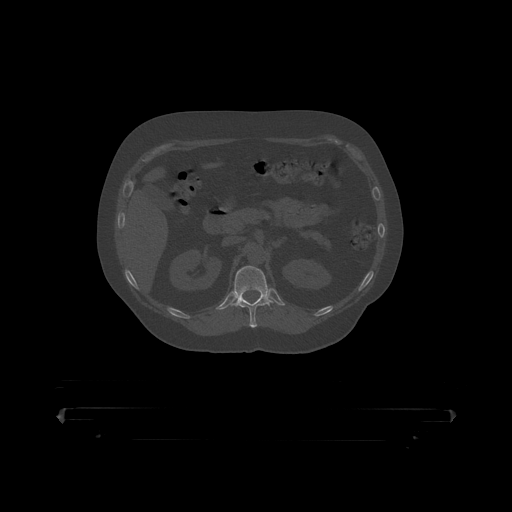
CT including the spine, one axial slice; slice 170 of 390 in the series (ordered by position); reconstruction kernel STANDARD; bone window (W 1800 / L 400 HU); 1.25 mm slice thickness; 512 × 512 image matrix. Patient: male, 60 years. From the clinical record (not read from this slice): primary cancer: prostate.
Outlined on this slice (semi-automatically segmented with operator editing):
- T12 vertebra: box from (x=231, y=266) to (x=274, y=319) px